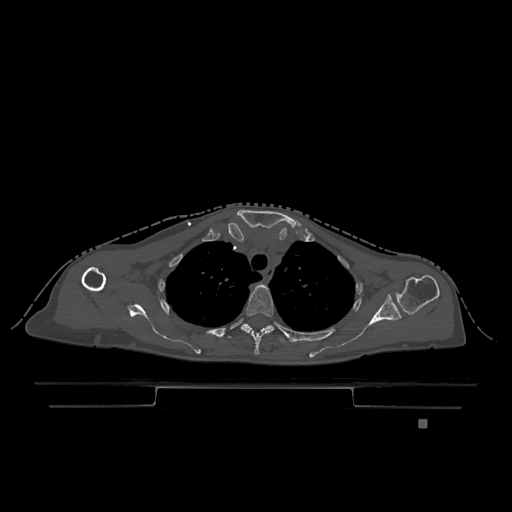
CT including the spine, one axial slice. Position 912 of 1317 along the scan axis. Bone window (W 1800 / L 400 HU). 0.5 mm slice thickness. 512 × 512 image matrix, field of view 500 × 500 mm. Female patient, age 74 years. From the clinical record (not read from this slice): primary cancer: lung; vertebrae with lytic lesions (as recorded): T1, T4, T5, T6, L4, L5.
Annotated regions visible in this slice (semi-automatically segmented with operator editing):
- T3 vertebra: box from (x=240, y=285) to (x=274, y=355) px
- T4 vertebra: (x=228, y=323)–(x=307, y=343)